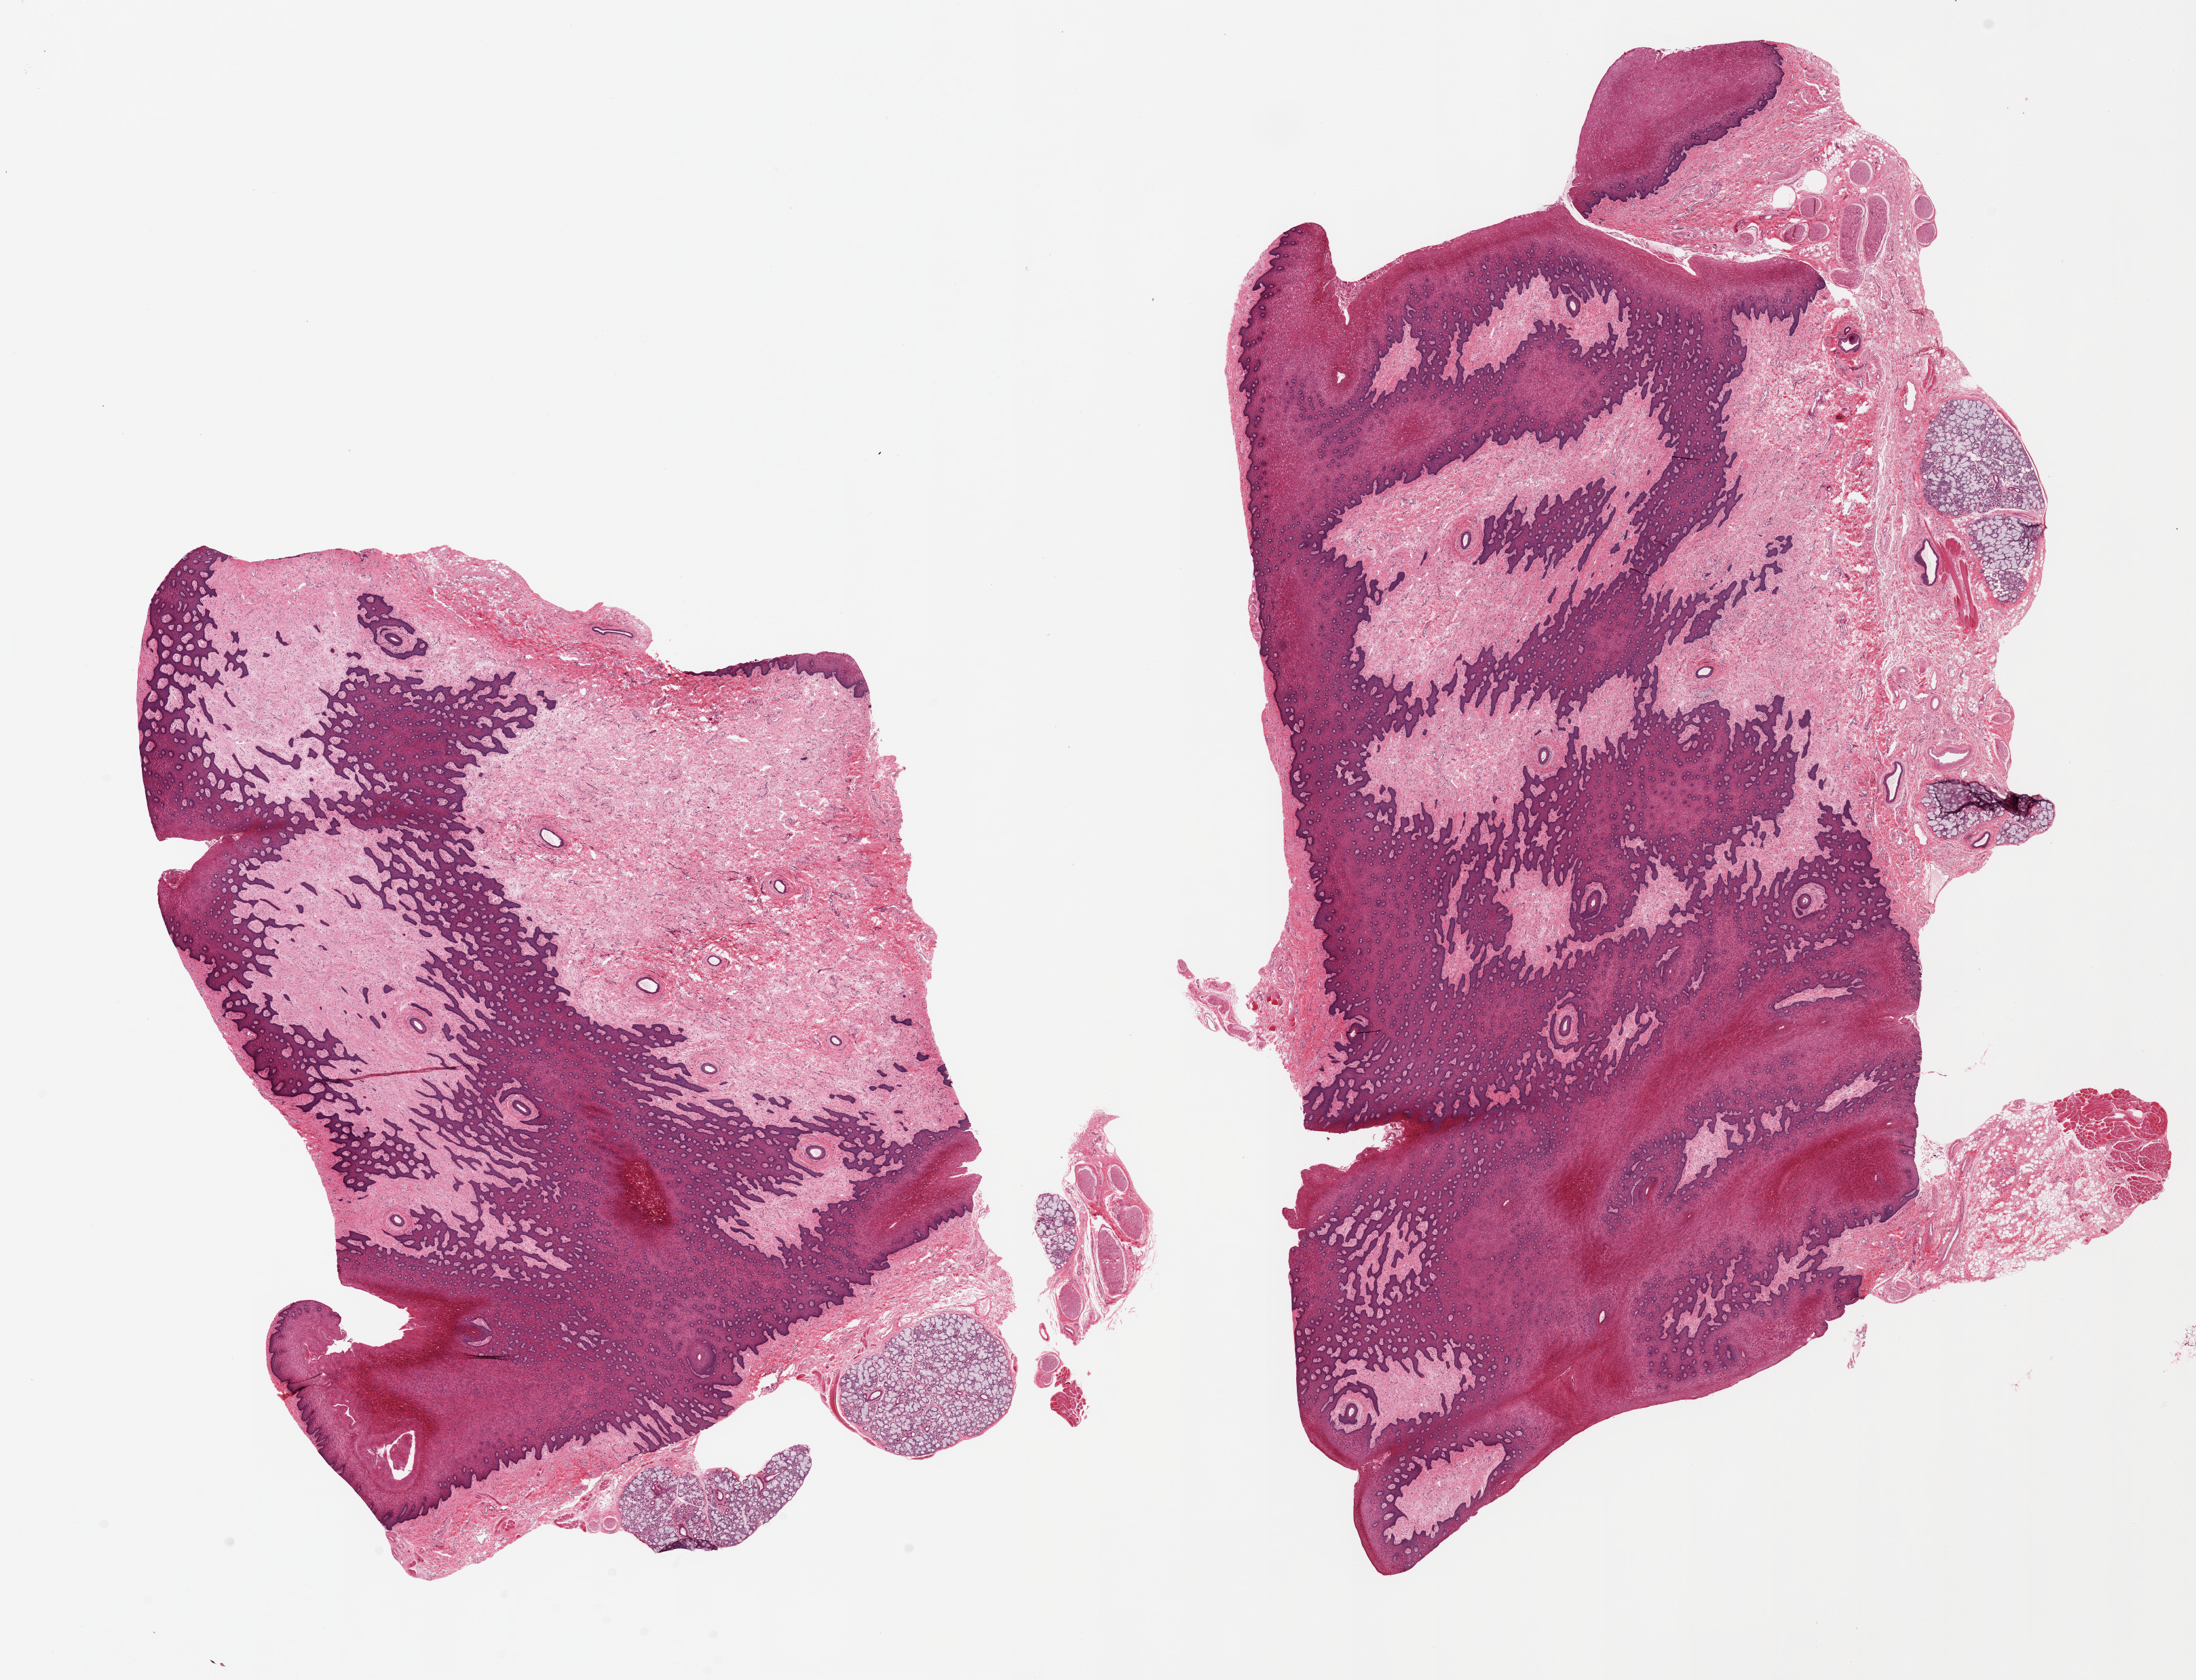
Whole-slide image, H&E stain — whole scanned area (about 25.6 x 19.6 mm) shown as a low-resolution overview. PAXgene-fixed paraffin-embedded (PFPE) section. Target tissue: minor salivary gland. Donor tissue sample. Male donor.
Reviewer comment on this tissue sample: 2 pieces; 5 small salivary glands around 2 mm in diameter attached to huge pieces of lip epithelium and stroma.